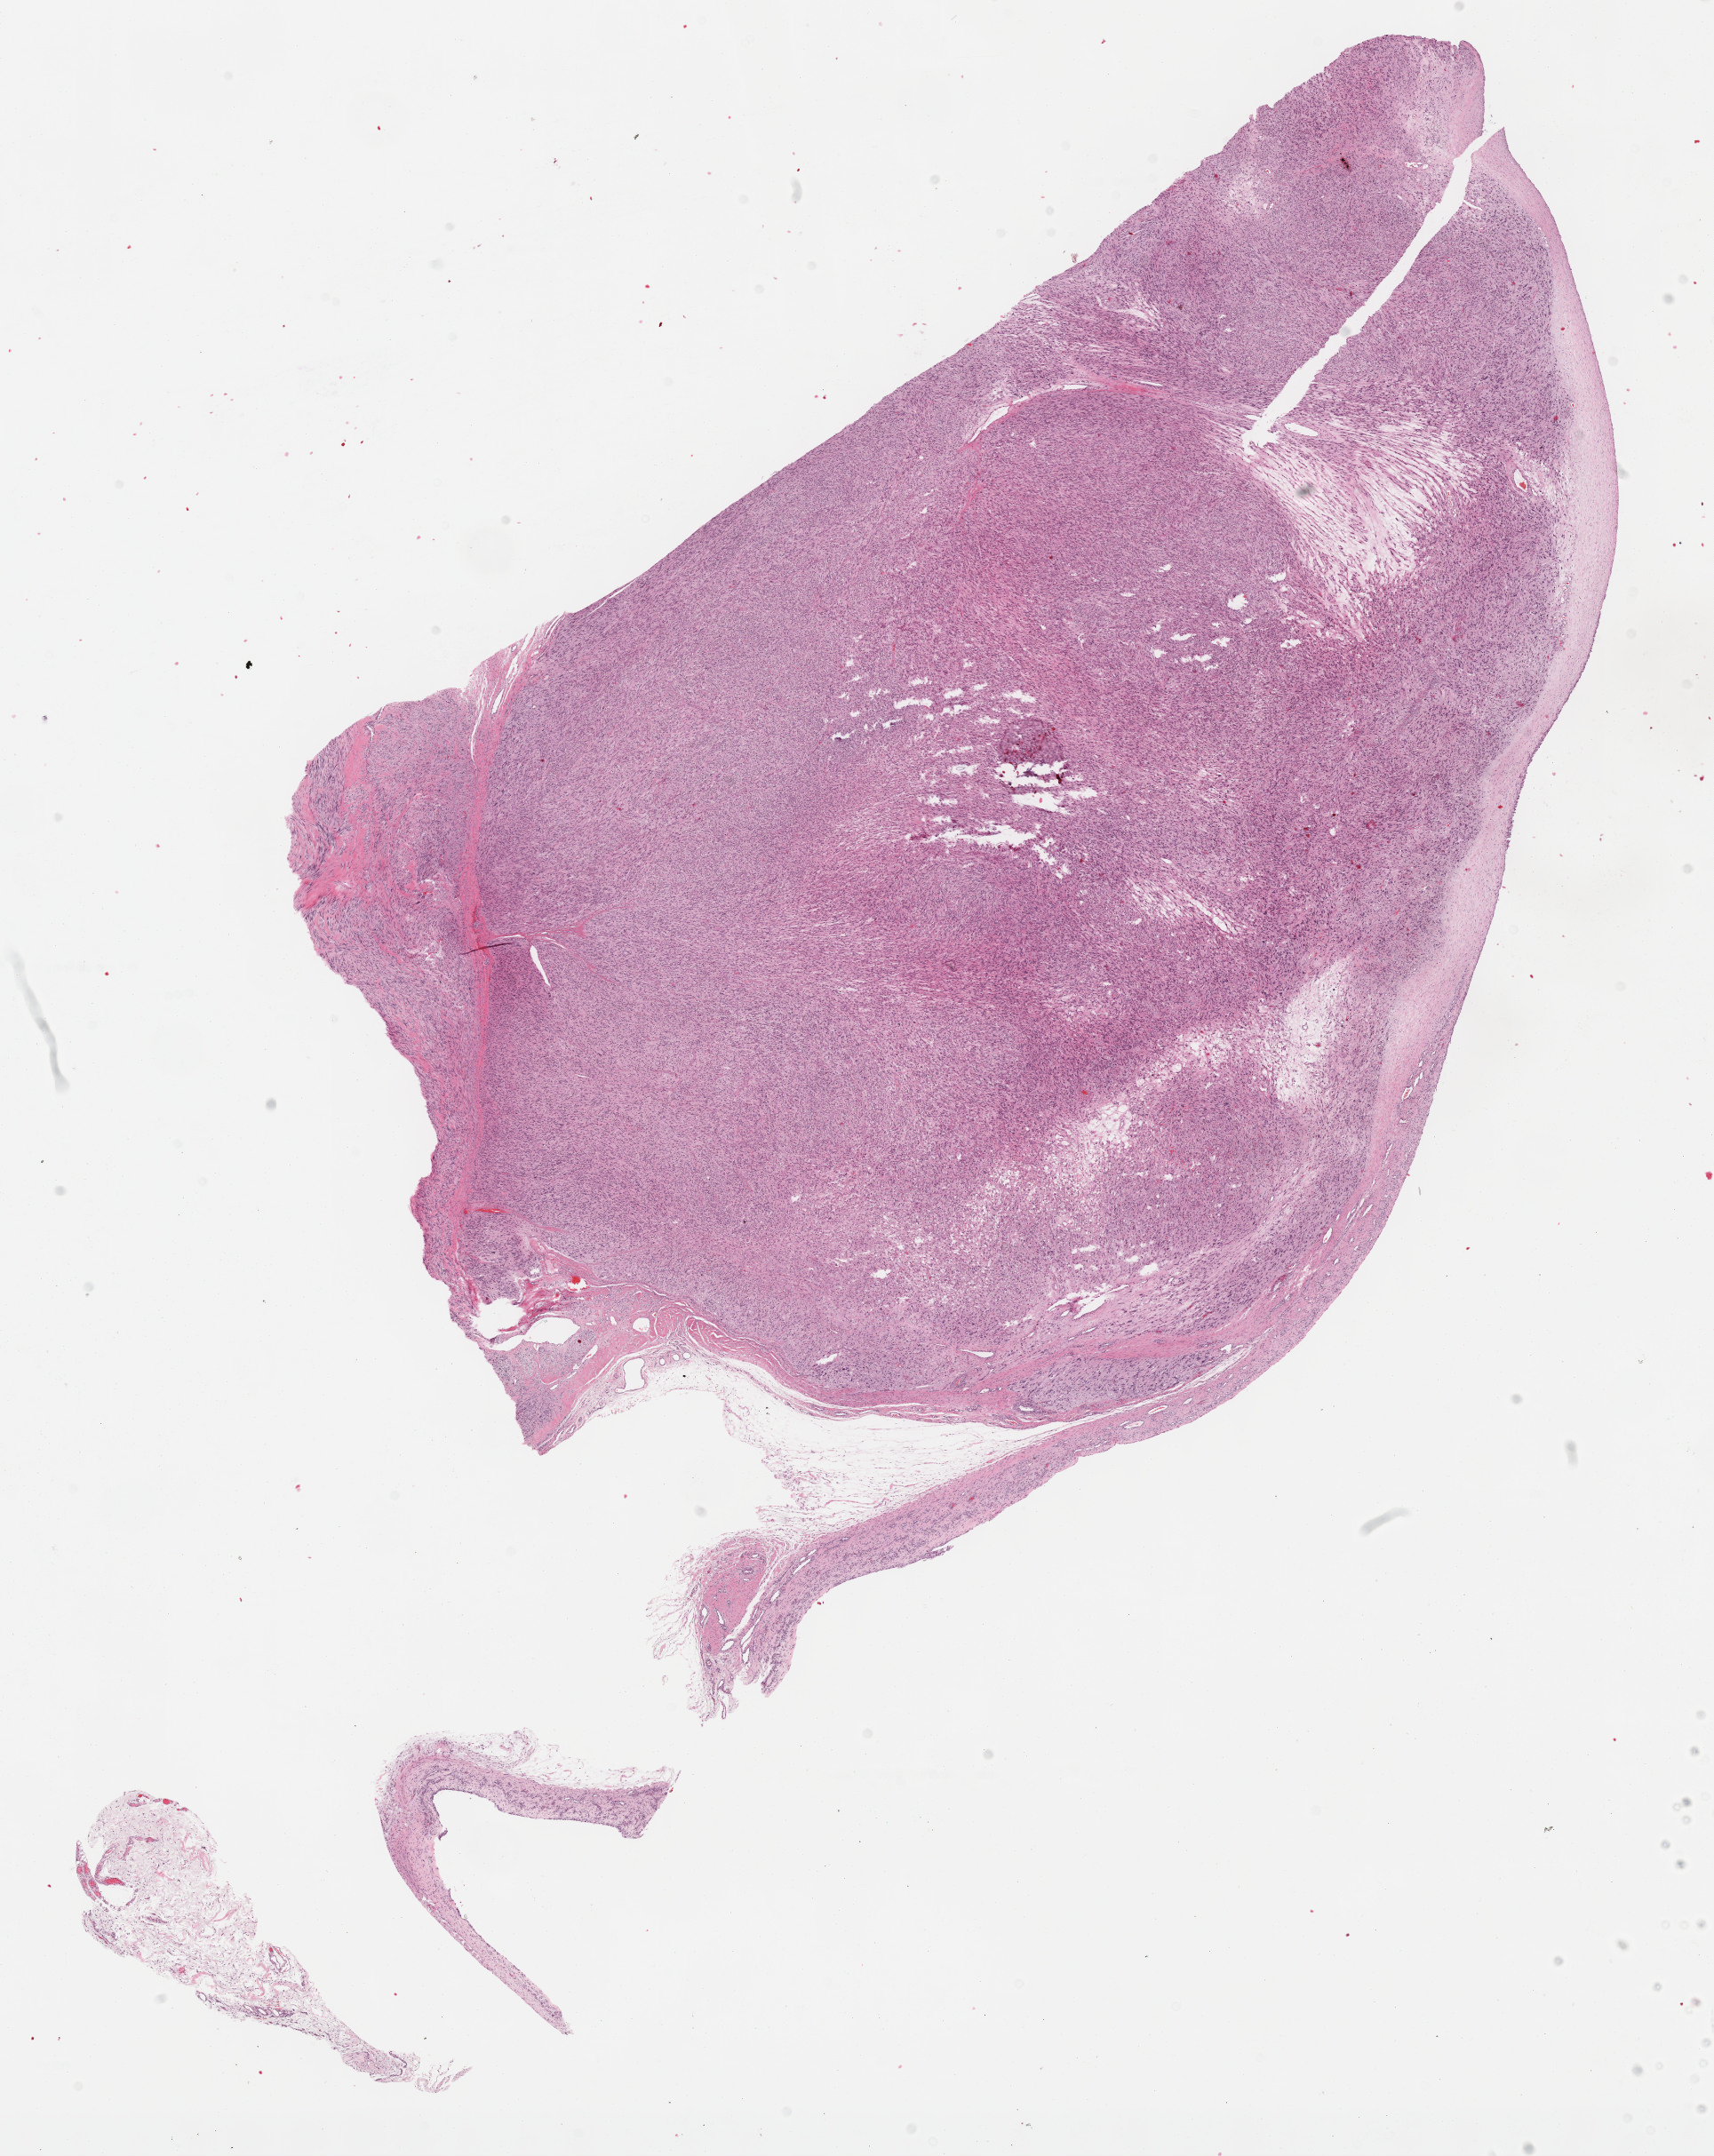
Hematoxylin and eosin (H&E) stained whole-slide image — whole scanned area (about 15.6 x 19.6 mm) shown as a low-resolution overview. Formalin-fixed paraffin-embedded (FFPE) diagnostic section. Primary tumour sample from the connective, subcutaneous and other soft tissues. Patient: female, age at initial diagnosis 49 years.
• pathologic diagnosis: Leiomyosarcoma, NOS (connective, subcutaneous and other soft tissues of lower limb and hip)